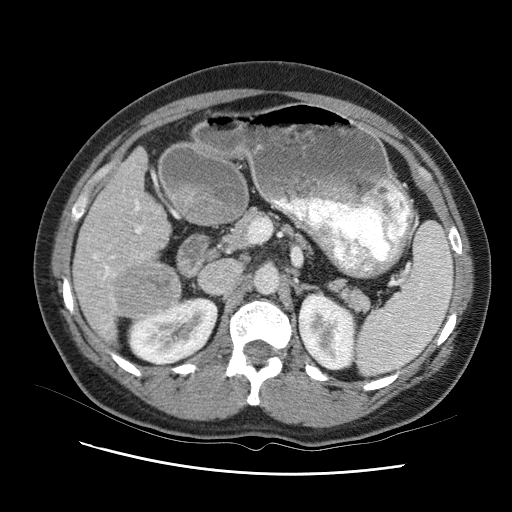
Contrast-enhanced abdominal CT (liver protocol), one axial slice; position 45 of 95 along the scan axis; reconstruction kernel STANDARD; 120 kVp; one of 2 acquisitions stored at this slice position; soft-tissue window (W 400 / L 40 HU); 2.5 mm slice thickness; 512 × 512 image matrix, field of view 360 × 360 mm. Case-level facts recorded for this patient, not image findings: diagnosis: hepatocellular carcinoma (patient treated with transarterial chemoembolisation; whether this scan precedes or follows treatment is not stated here); TNM stage (as recorded): Stage-I; Child-Pugh class: B; tumour nodularity: uninodular.
Outlined on this slice (semi-automatic segmentation, software-assisted and operator-edited):
- liver parenchyma outside the tumour (the mass and vessels are separate outlines, so this box may not span the whole liver): bounding box [x1, y1, x2, y2] px = [72, 138, 181, 360]
- mass: [118, 249, 186, 313]
- liver vessels: [103, 193, 168, 338]